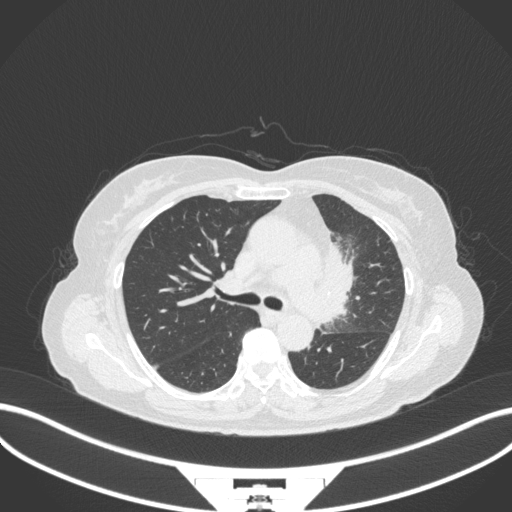
Chest CT, one axial slice; slice 213 of 382 in the series (ordered by position); reconstruction kernel B31f; 120 kVp; lung window (W 1500 / L -600 HU); 1 mm slice thickness; 512 × 512 image matrix, field of view 400 × 400 mm. Patient: female, 64 years. From the clinical record (not read from this slice): clinical TNM (as recorded): T2a N2 M0.
Structures marked on this image (rectangle marked by the reading radiologist):
- lung tumour (recorded histology: adenocarcinoma): bounding box [x1, y1, x2, y2] px = [322, 241, 362, 317]